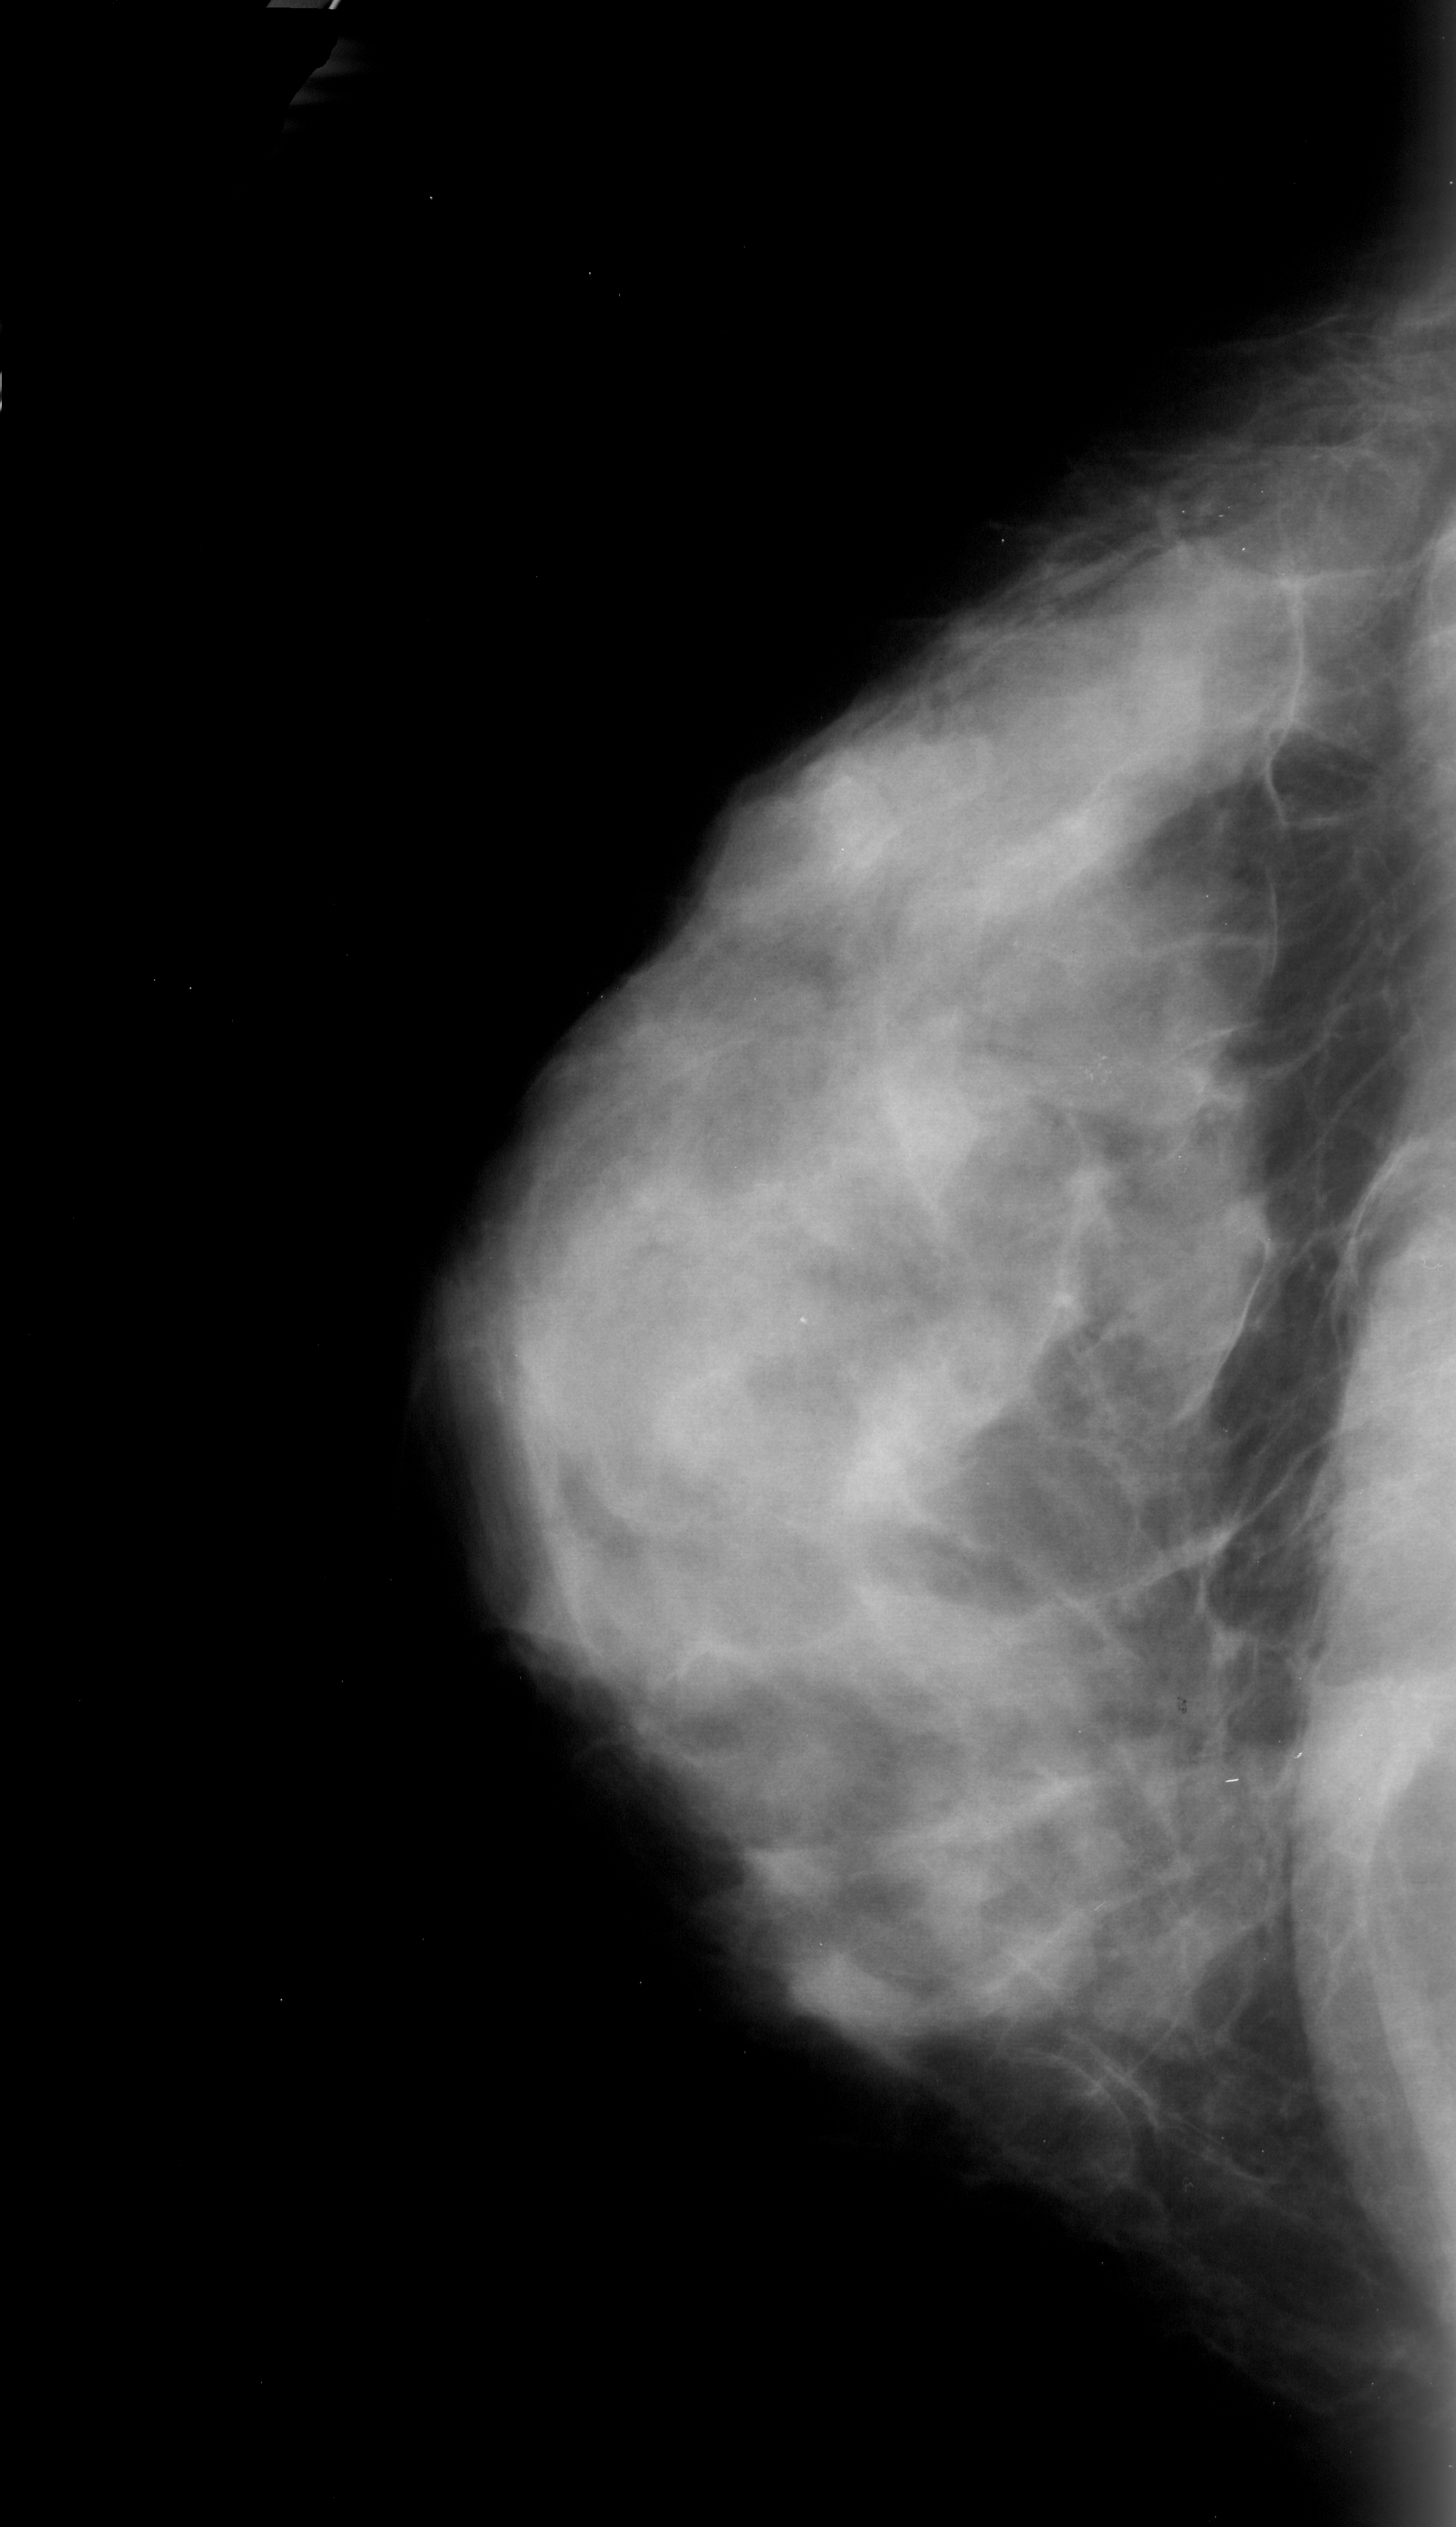
Scanned film-screen mammogram; left breast; craniocaudal (CC) view; BI-RADS breast density category 4 (scale 1–4); 1456 × 2527 image matrix.
Expert-marked regions of interest on this image (one box per marked abnormality):
- calcifications, morphology punctate, distribution clustered; BI-RADS assessment category 4; subtlety rating 1 on a 1 (subtle) to 5 (obvious) scale; pathology result (as recorded, not read from the image): malignant: bounding box (x1, y1, x2, y2) in pixels: (1062, 1037, 1135, 1107)